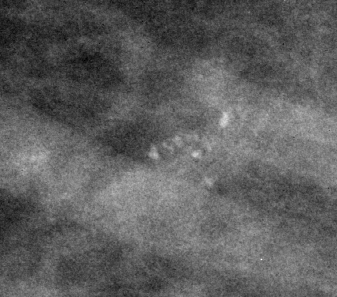
Crop from a digitized film mammogram around one marked abnormality, right breast, MLO view, BI-RADS breast density category 1 (scale 1–4).
Finding: calcifications, morphology pleomorphic, distribution clustered; BI-RADS assessment category 4; pathology (as recorded): benign.